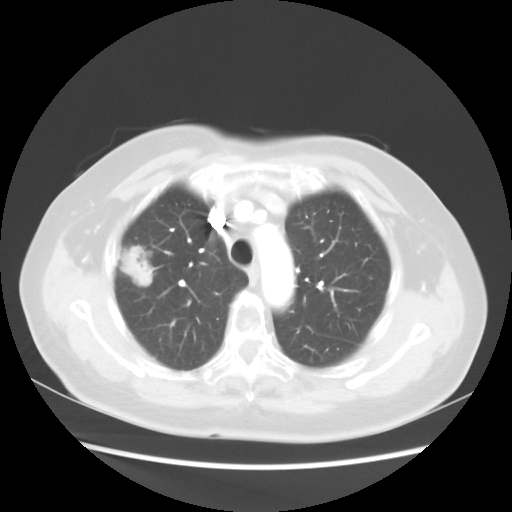
Chest CT, one axial slice; position 36 of 48 along the scan axis; reconstruction kernel STANDARD; lung window (W 1500 / L -600 HU); 5 mm slice thickness; 512 × 512 image matrix, field of view 360 × 360 mm. Female patient, age 75 years. From the clinical record (not read from this slice): clinical TNM (as recorded): T1c N0 M0.
Structures marked on this image (bounding box drawn by a radiologist):
- lung tumour (recorded histology: adenocarcinoma): box from (x=125, y=243) to (x=159, y=289) px